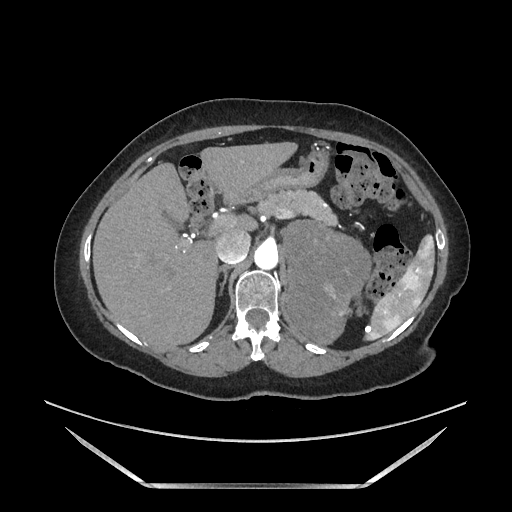
Contrast-enhanced abdominal CT, one axial slice. Position 118 of 205 along the scan axis. Soft-tissue window (W 400 / L 40 HU). 1.25 mm slice thickness. 512 × 512 image matrix, field of view 440 × 440 mm. Female patient. Case-level facts recorded for this patient, not image findings: diagnosis: adrenocortical carcinoma; tumour side: left adrenal; tumour size at pathology: 12.5 cm; Ki-67 index: 39 %; stage (as recorded): 3.
Annotated regions visible in this slice (semi-automatic segmentation, software-assisted and operator-edited):
- mass: bounding box [x1, y1, x2, y2] px = [289, 223, 370, 343]